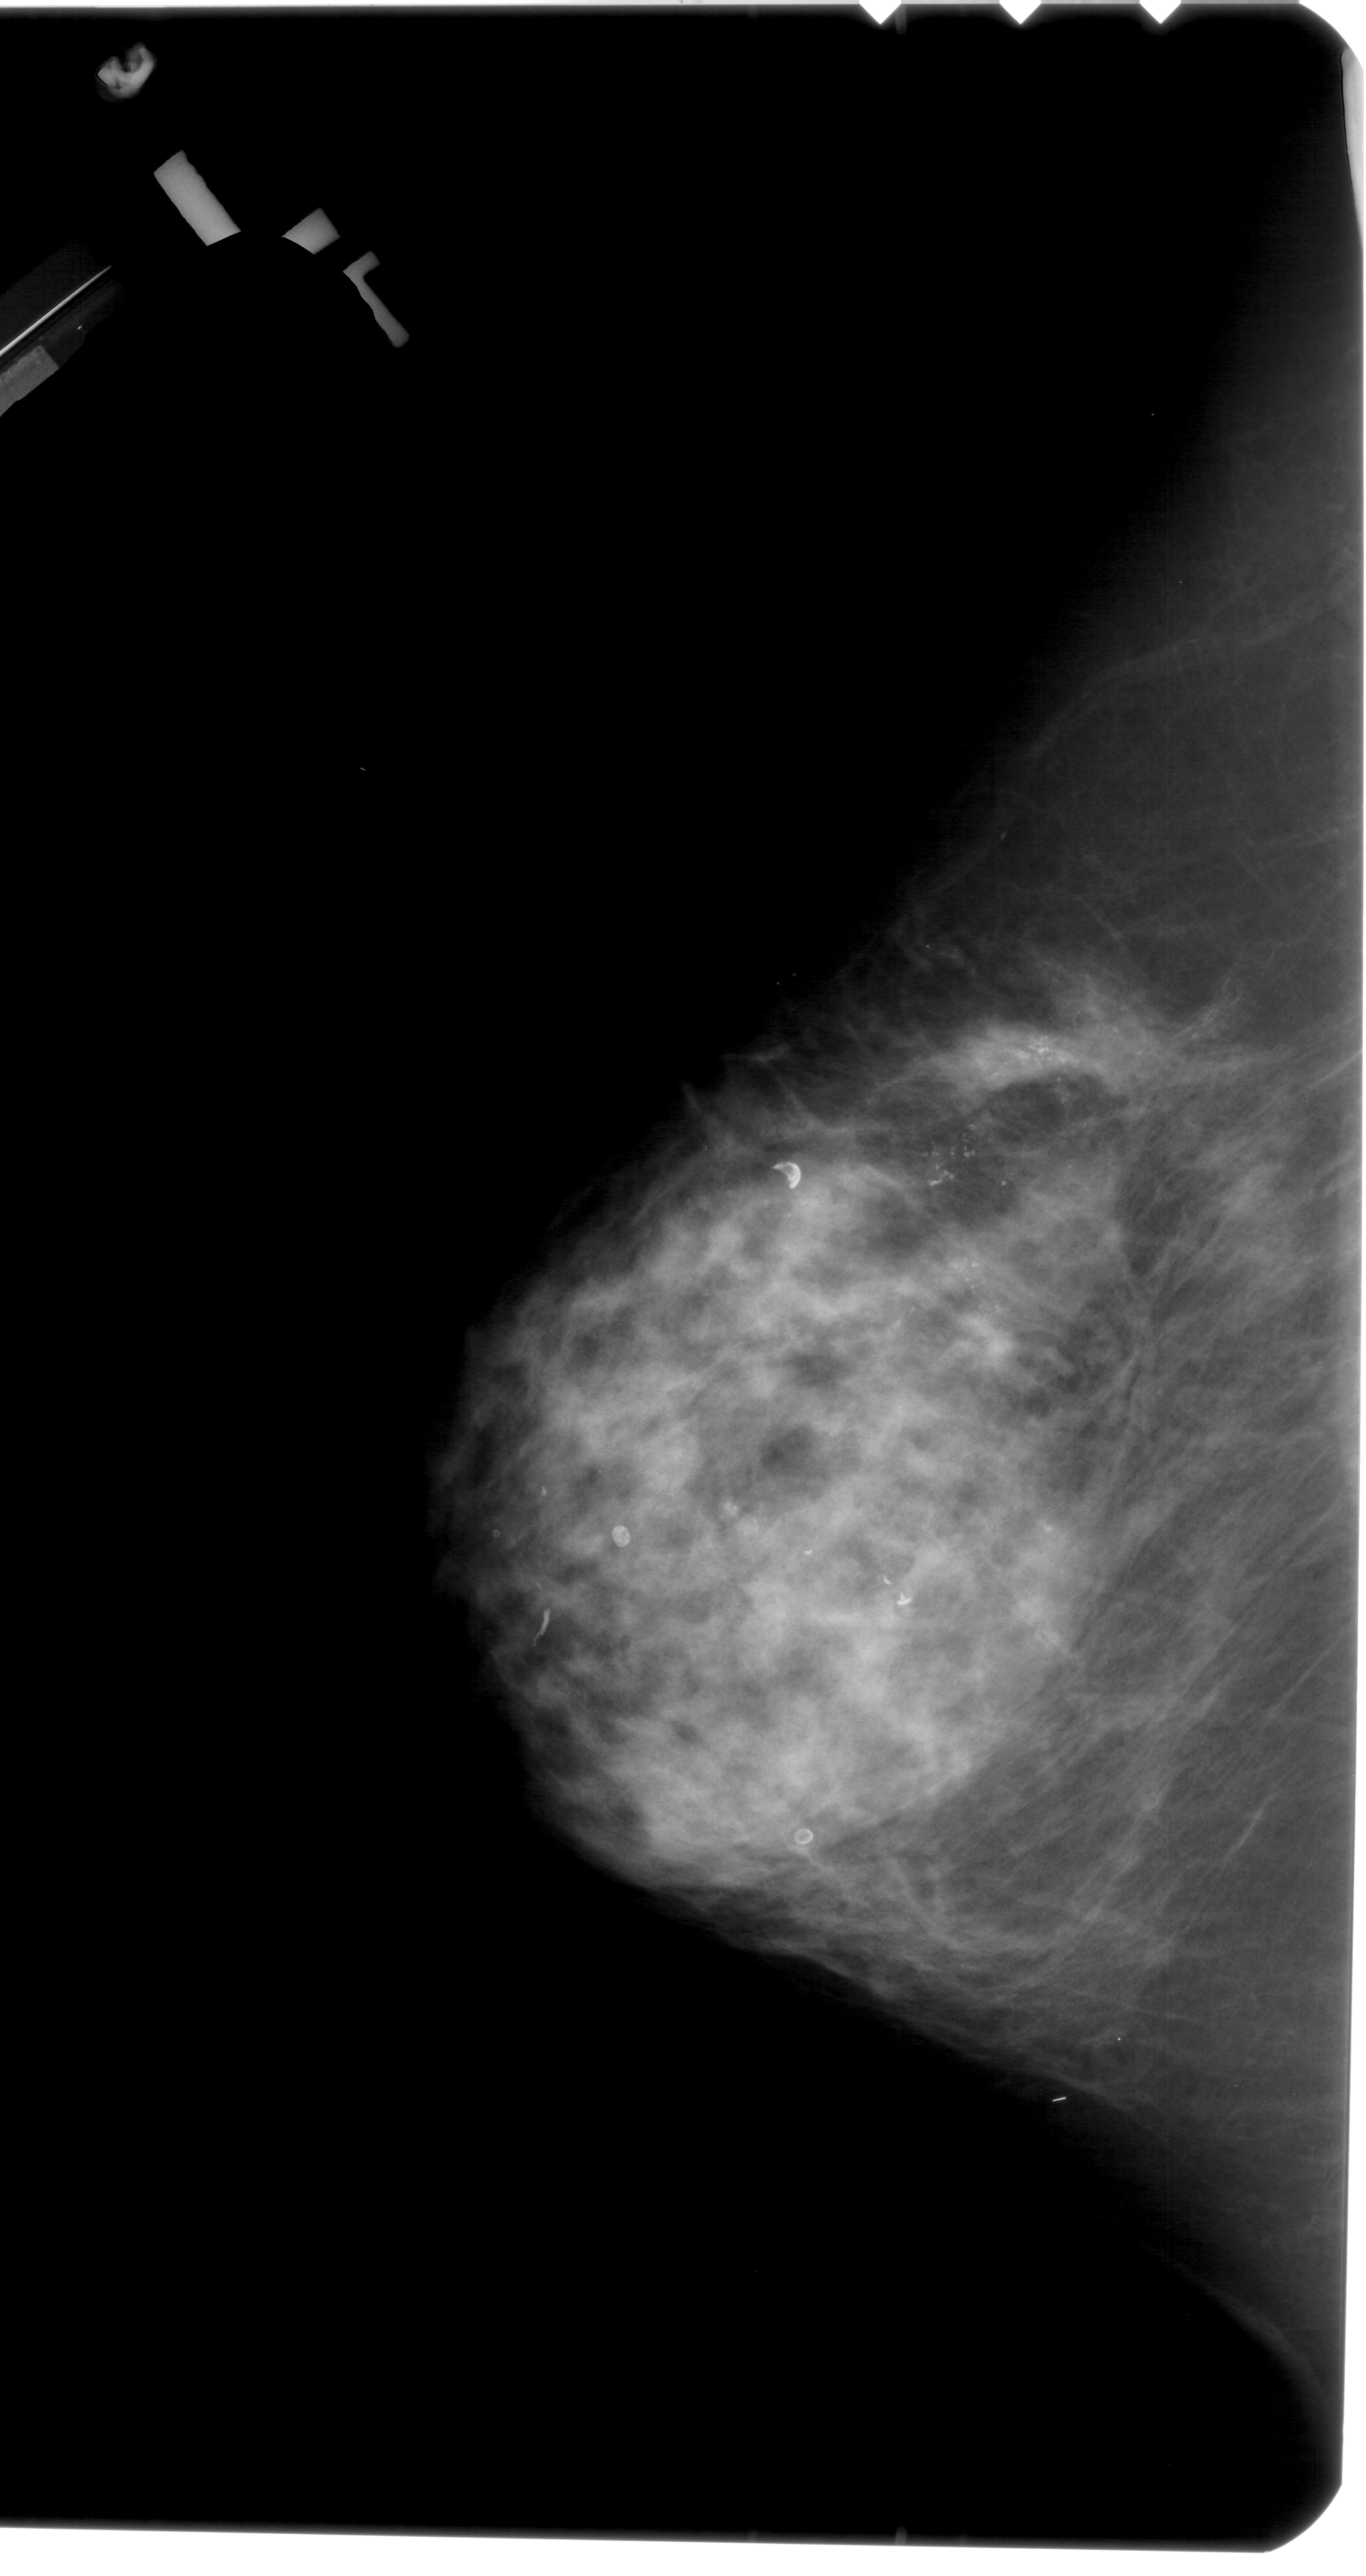
Scanned film-screen mammogram; left breast; craniocaudal (CC) view; BI-RADS breast density category 4 (scale 1–4).
- Calcifications, morphology pleomorphic, distribution regional; BI-RADS assessment category 5; pathology (as recorded): malignant.